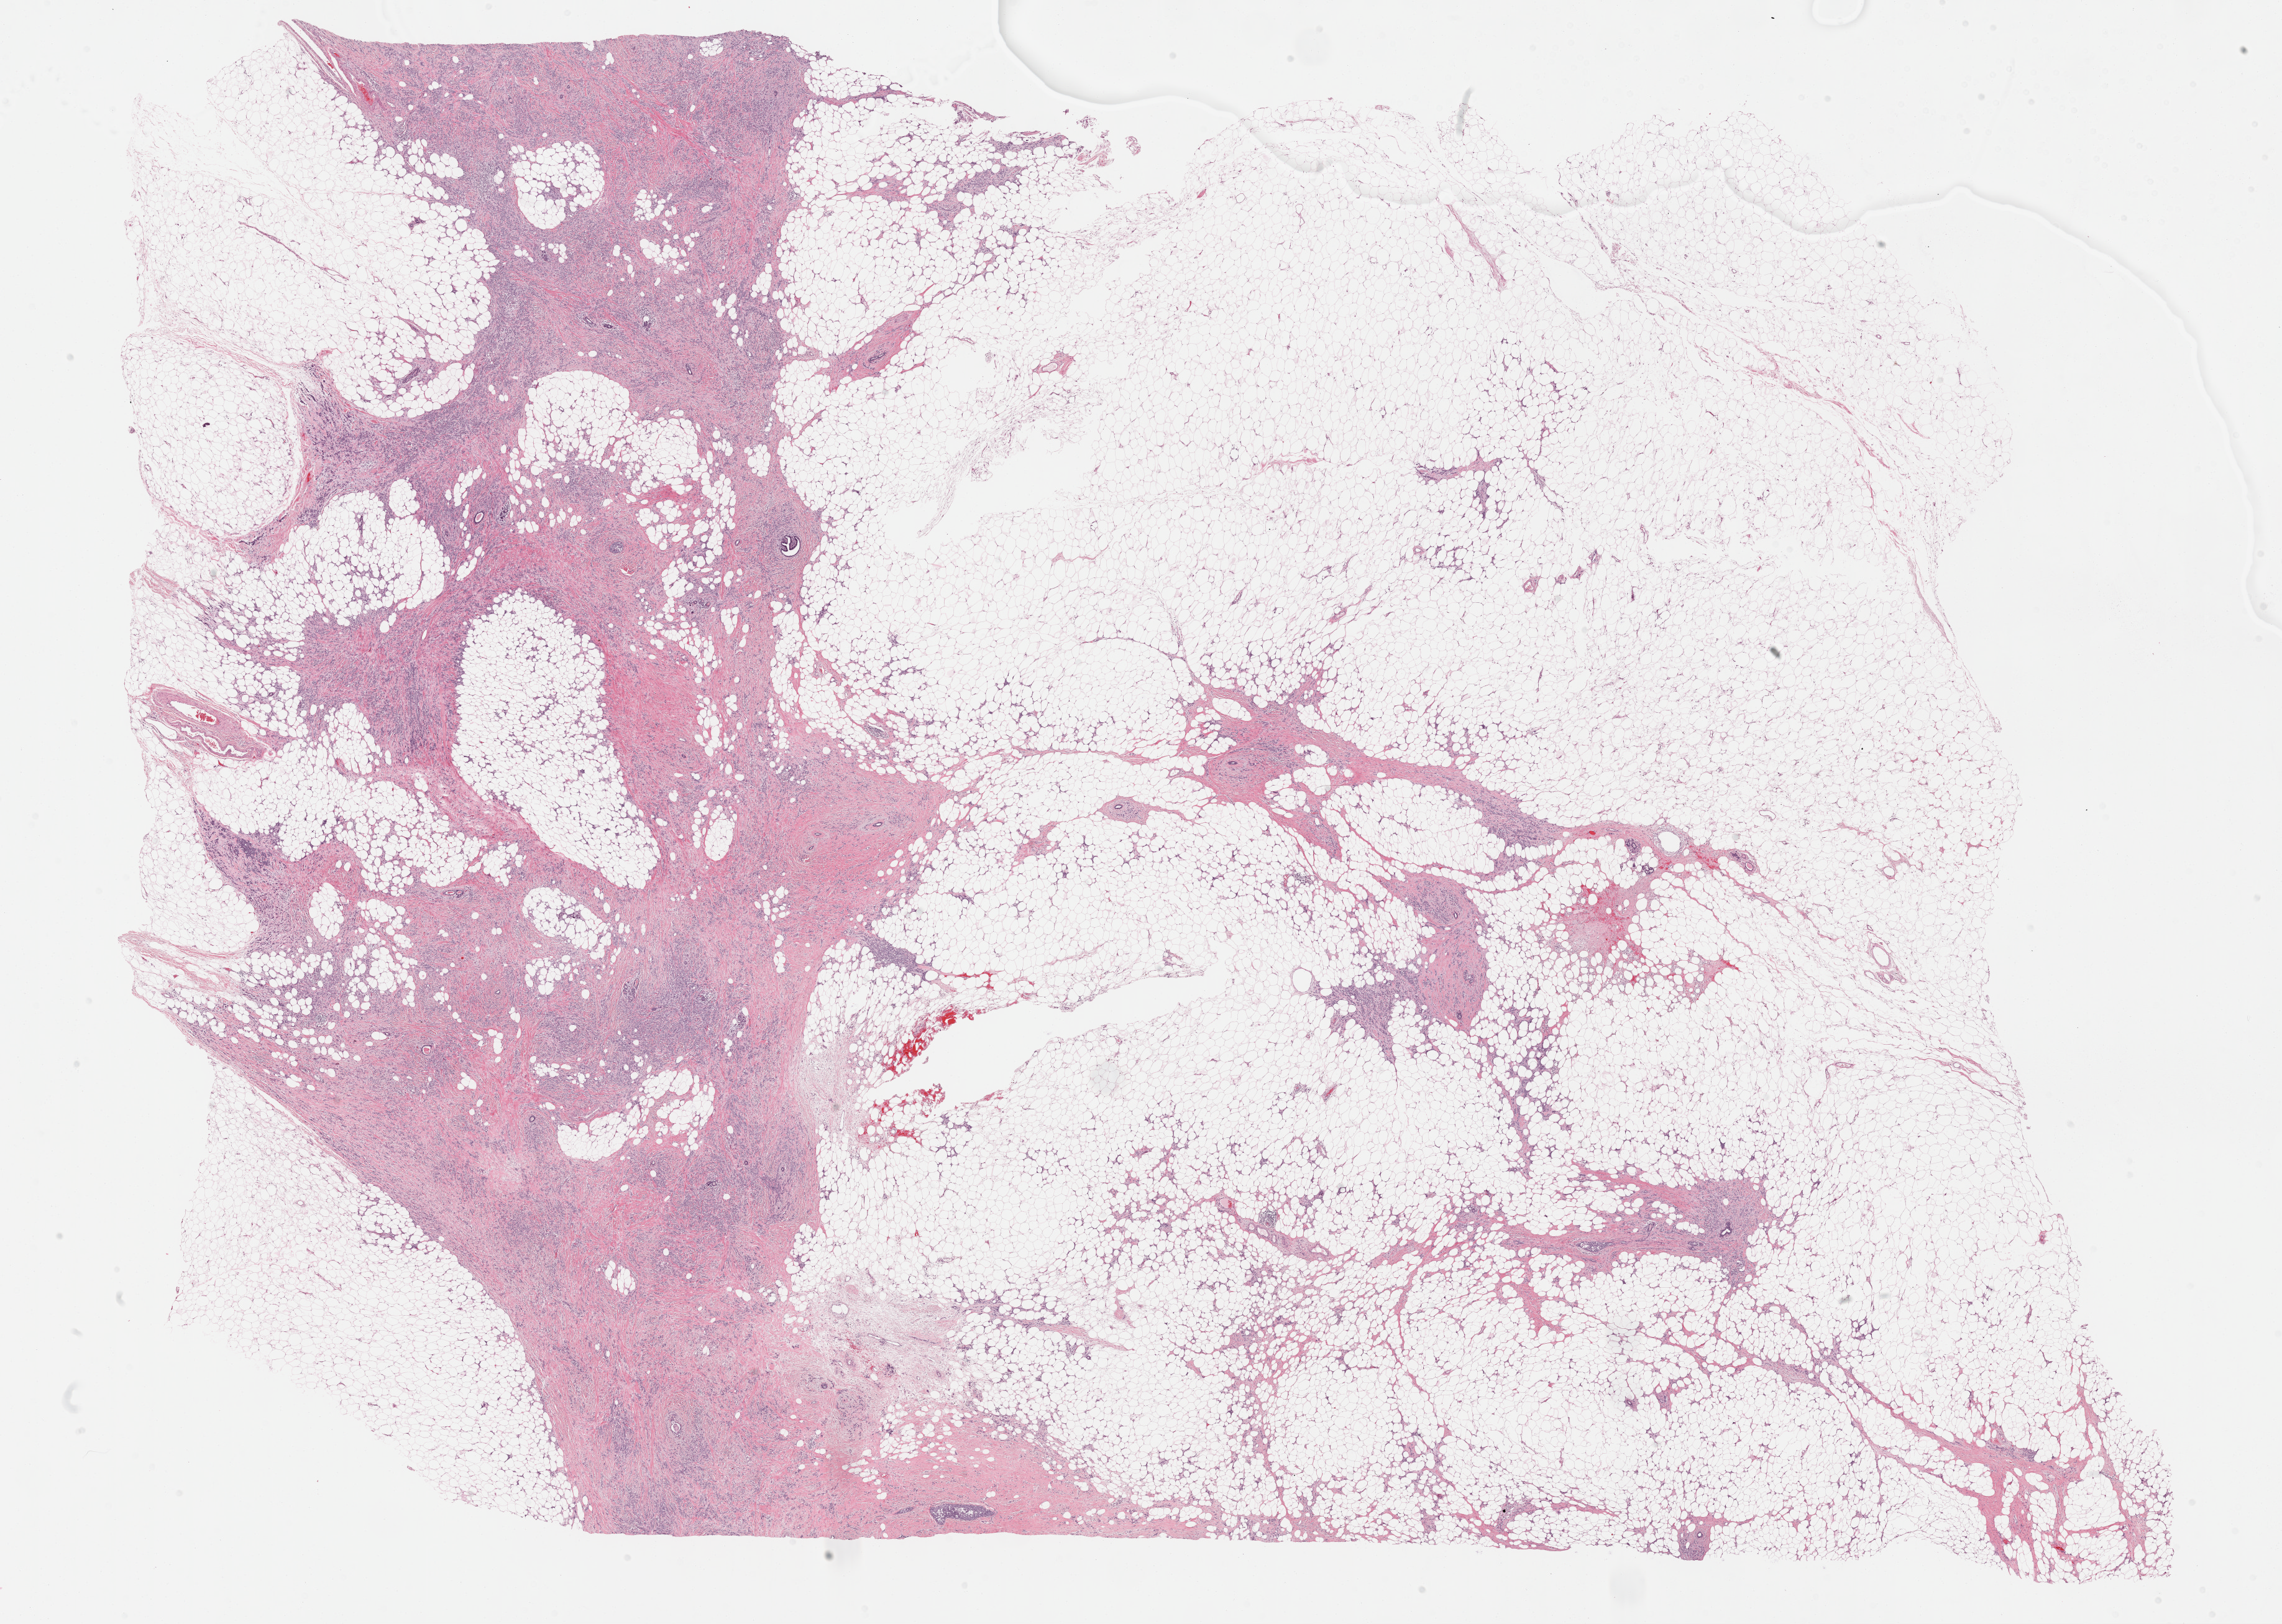
Digitized H&E tissue section (whole slide) — whole scanned area (about 29.7 x 21.1 mm, from a 40x scan) shown as a low-resolution overview; formalin-fixed paraffin-embedded (FFPE) diagnostic section; primary tumour sample from the breast. Female, age 68 years at initial diagnosis.
* AJCC pathologic stage: IIB (7th edition)
* TNM: T3 N0 MX
* diagnosis: Lobular carcinoma, NOS